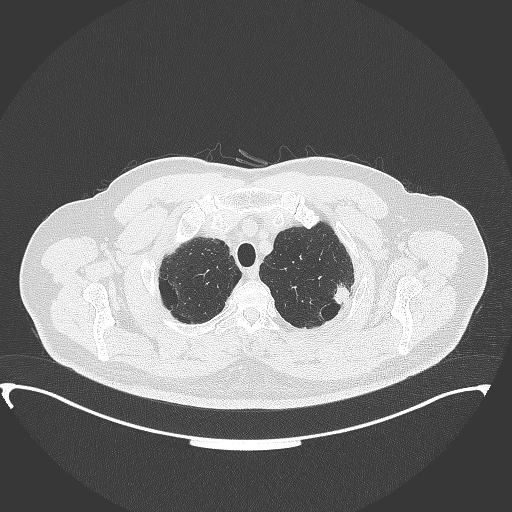
Chest CT, one axial slice; slice 320 of 350 in the series (ordered by position); 120 kVp; lung window (W 1500 / L -600 HU); 1 mm slice thickness; 512 × 512 image matrix. Male patient, age 64 years. Case-level facts recorded for this patient, not image findings: clinical TNM (as recorded): T1c N1 M1.
Outlined on this slice (bounding box drawn by a radiologist):
- lung tumour (recorded histology: adenocarcinoma): bounding box (x1, y1, x2, y2) in pixels: (331, 281, 355, 308)